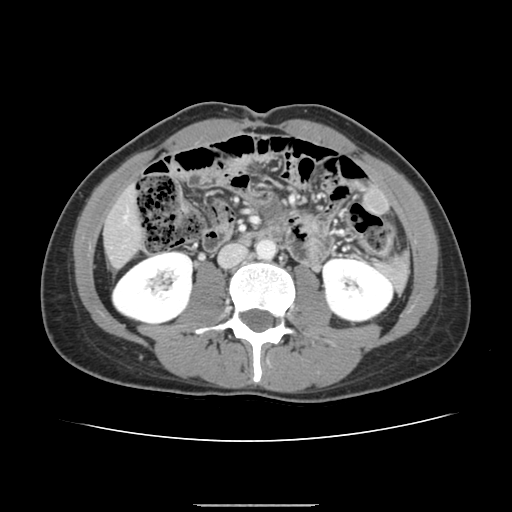
Contrast-enhanced abdominal CT, one axial slice. Slice 41 of 150 in the series (ordered by position). Intravenous contrast given. Soft-tissue window (W 400 / L 40 HU). 2.5 mm slice thickness. 512 × 512 image matrix, field of view 324 × 324 mm. Female patient, age 32 years. Case-level facts recorded for this patient, not image findings: diagnosis: colorectal cancer liver metastases, imaged before liver resection; multiple liver metastases: yes.
Outlined on this slice (outlined manually by an expert reader):
- liver: box from (x=105, y=191) to (x=142, y=266) px
- planned liver remnant (the part of the liver to remain after resection): (x=105, y=191)–(x=142, y=267)